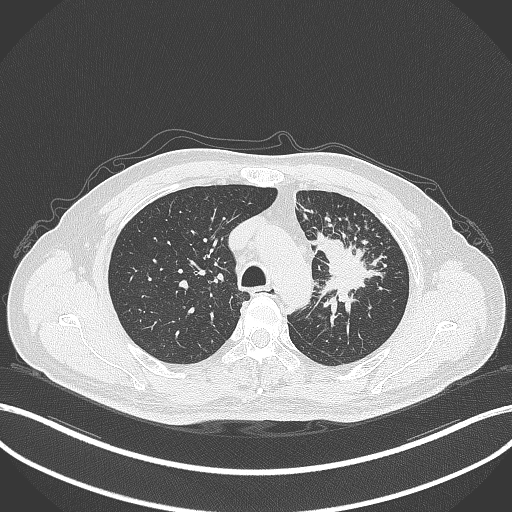
Chest CT, one axial slice. Position 265 of 386 along the scan axis. 120 kVp. Lung window (W 1500 / L -600 HU). 512 × 512 image matrix. Male patient, age 69 years. Case-level facts recorded for this patient, not image findings: clinical TNM (as recorded): T2a N2 M0.
Structures marked on this image (rectangle marked by the reading radiologist):
- lung tumour (recorded histology: adenocarcinoma): box from (x=311, y=224) to (x=387, y=318) px